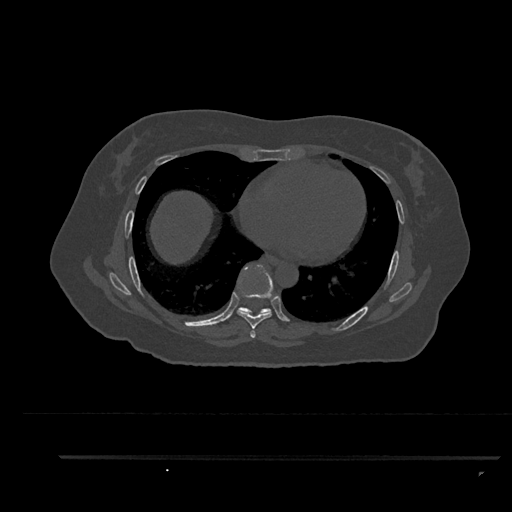
CT including the spine, one axial slice; slice 493 of 797 in the series (ordered by position); reconstruction kernel Br40s/3; bone window (W 1800 / L 400 HU); 0.5 mm slice thickness; 512 × 512 image matrix. Female patient, age 44 years. From the clinical record (not read from this slice): primary cancer: renal; vertebrae with lytic lesions (as recorded): L1.
Annotated regions visible in this slice (semi-automatic segmentation, software-assisted and operator-edited):
- T6 vertebra: bounding box <251,335,255,338> (left, top, right, bottom; pixels)
- T7 vertebra: <237,264,273,338>
- T8 vertebra: <238,274,271,316>